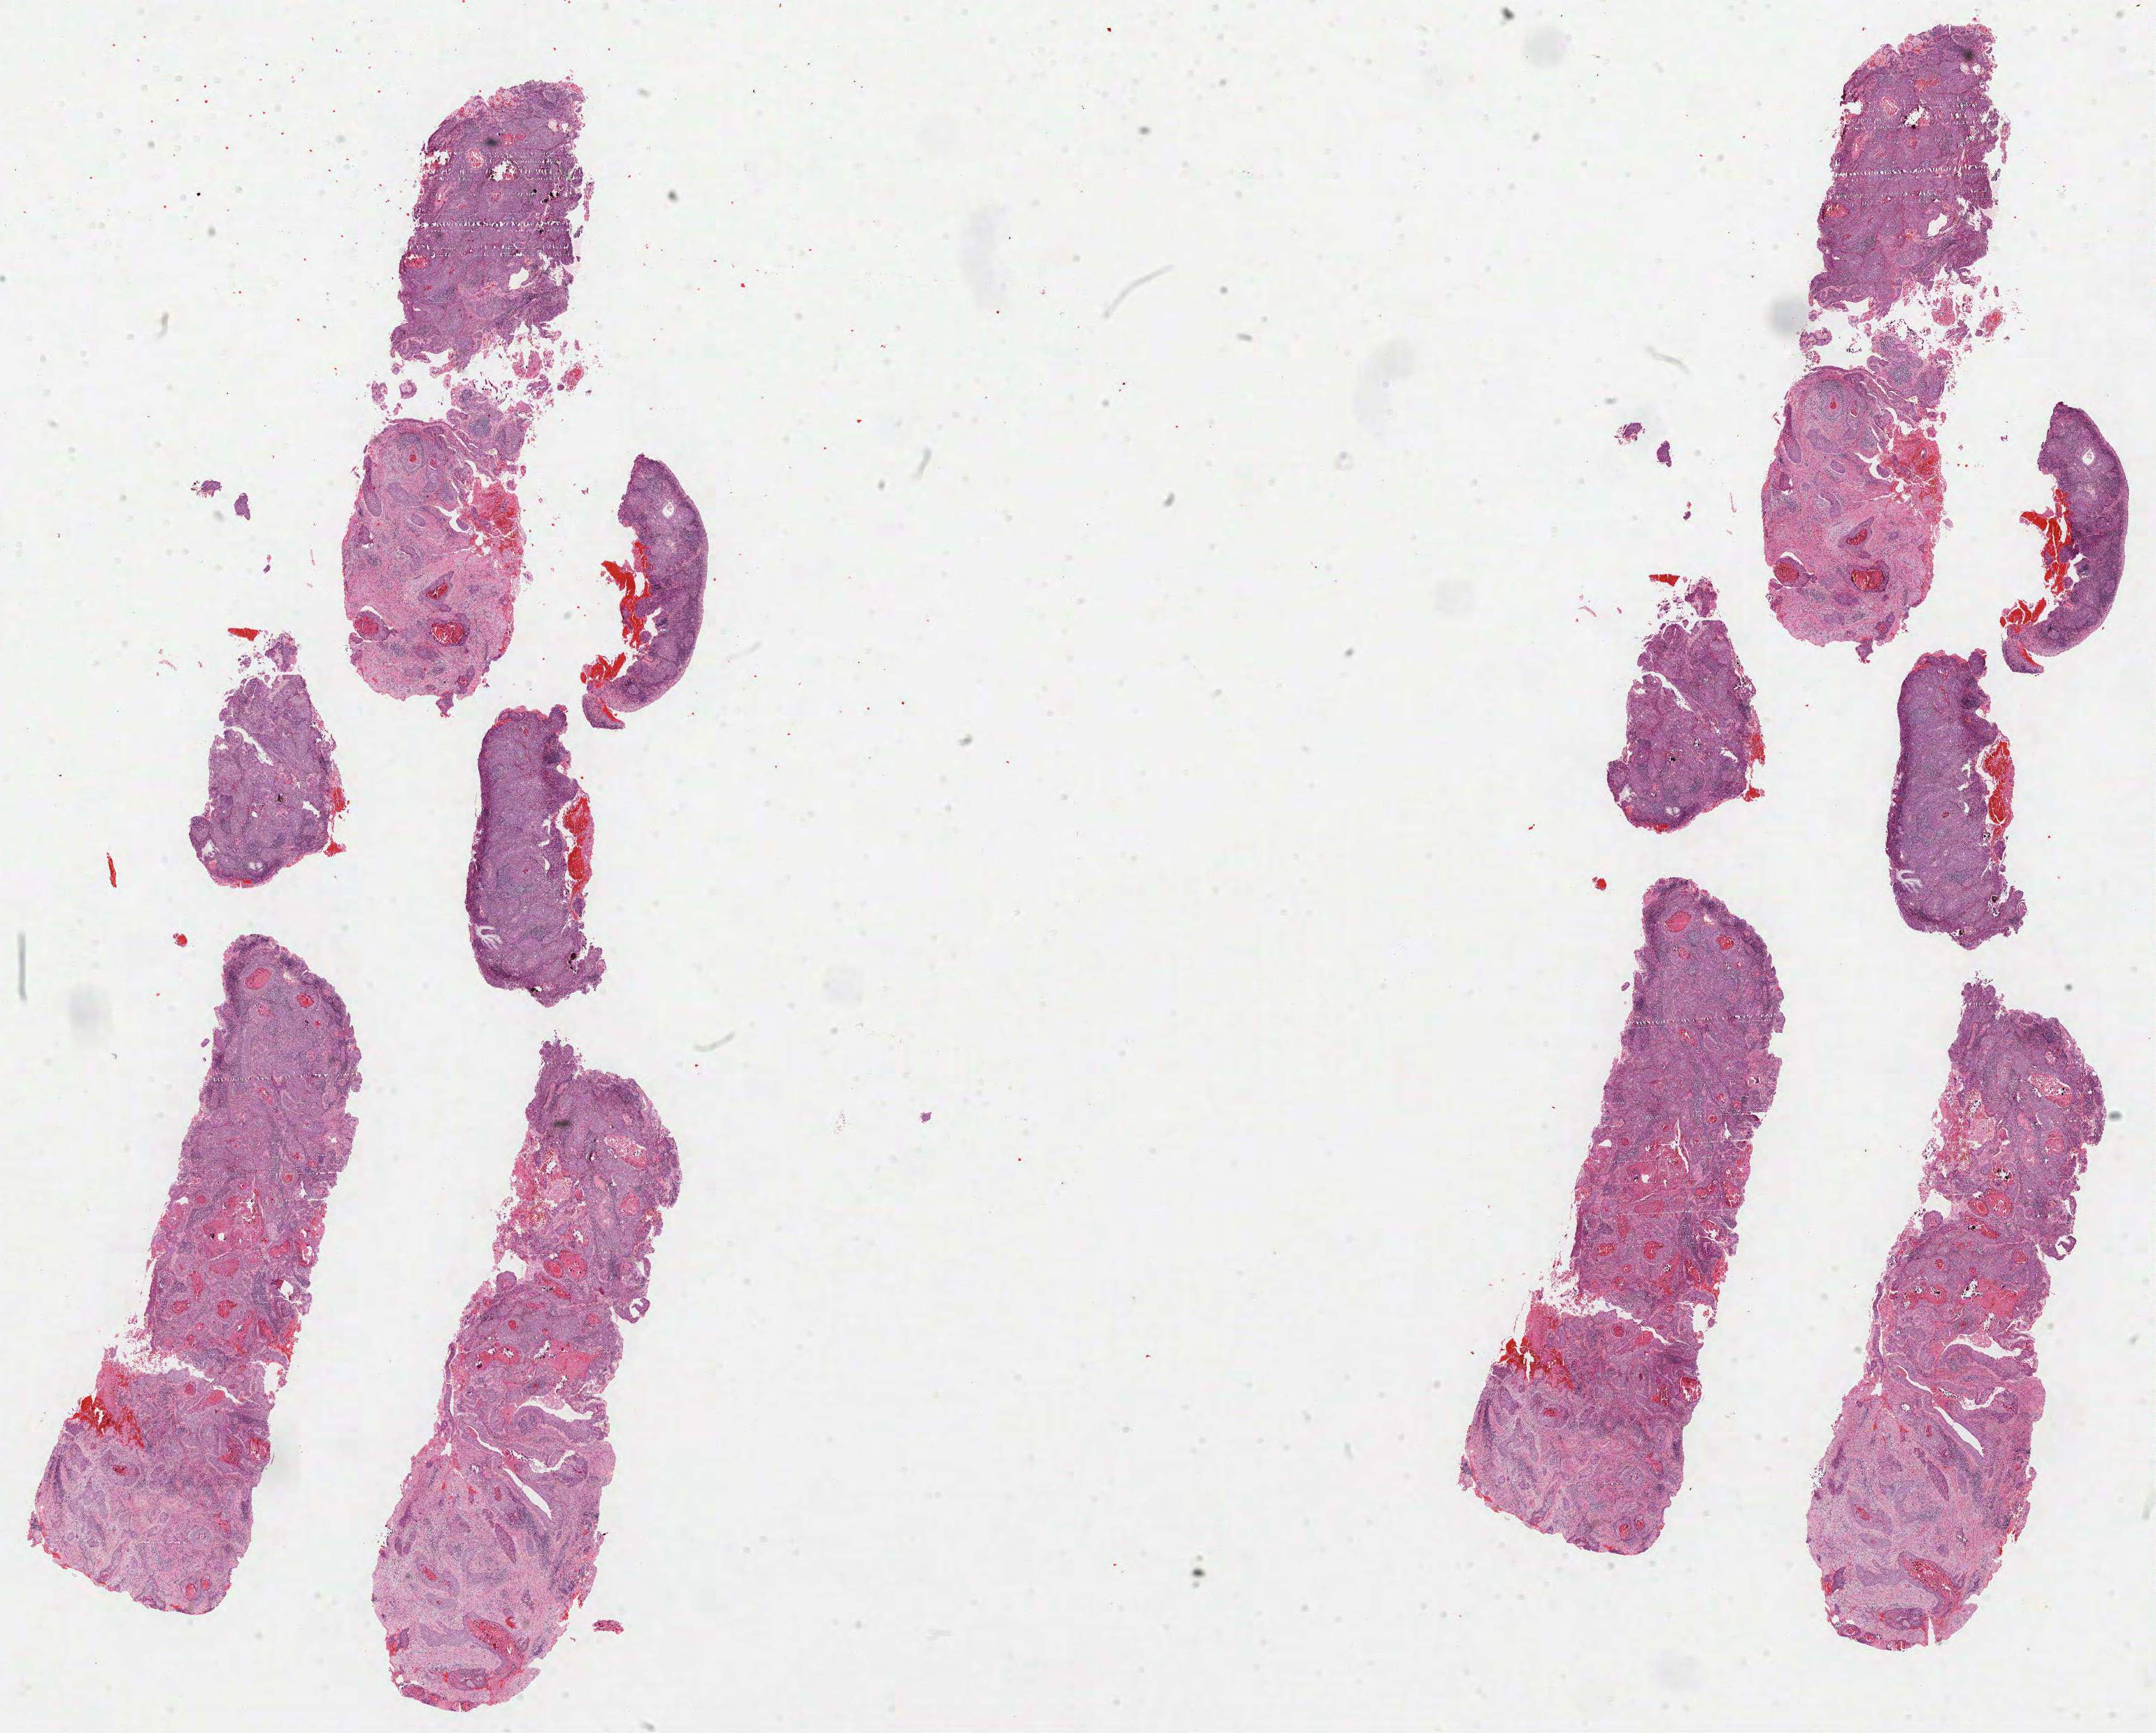
Digitized H&E tissue section (whole slide) — a low-resolution overview of the entire scanned area, about 24.8 x 20.0 mm (from a 40x scan); formalin-fixed paraffin-embedded (FFPE) diagnostic section; sample: primary tumour, cervix. Female, age 62 years at initial diagnosis.
Diagnosis: Squamous cell carcinoma, keratinizing, NOS.